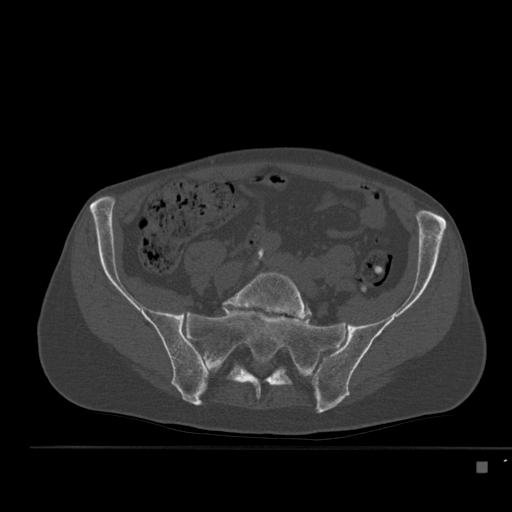
CT including the spine, one axial slice. Slice 110 of 517 in the series (ordered by position). 120 kVp. Bone window (W 1800 / L 400 HU). 1.5 mm slice thickness. 512 × 512 image matrix, field of view 408 × 408 mm. Patient: male, 70 years. Case-level facts recorded for this patient, not image findings: primary cancer: renal.
Outlined on this slice (semi-automatically segmented with operator editing):
- L5 vertebra: bounding box [x1, y1, x2, y2] px = [223, 271, 312, 320]